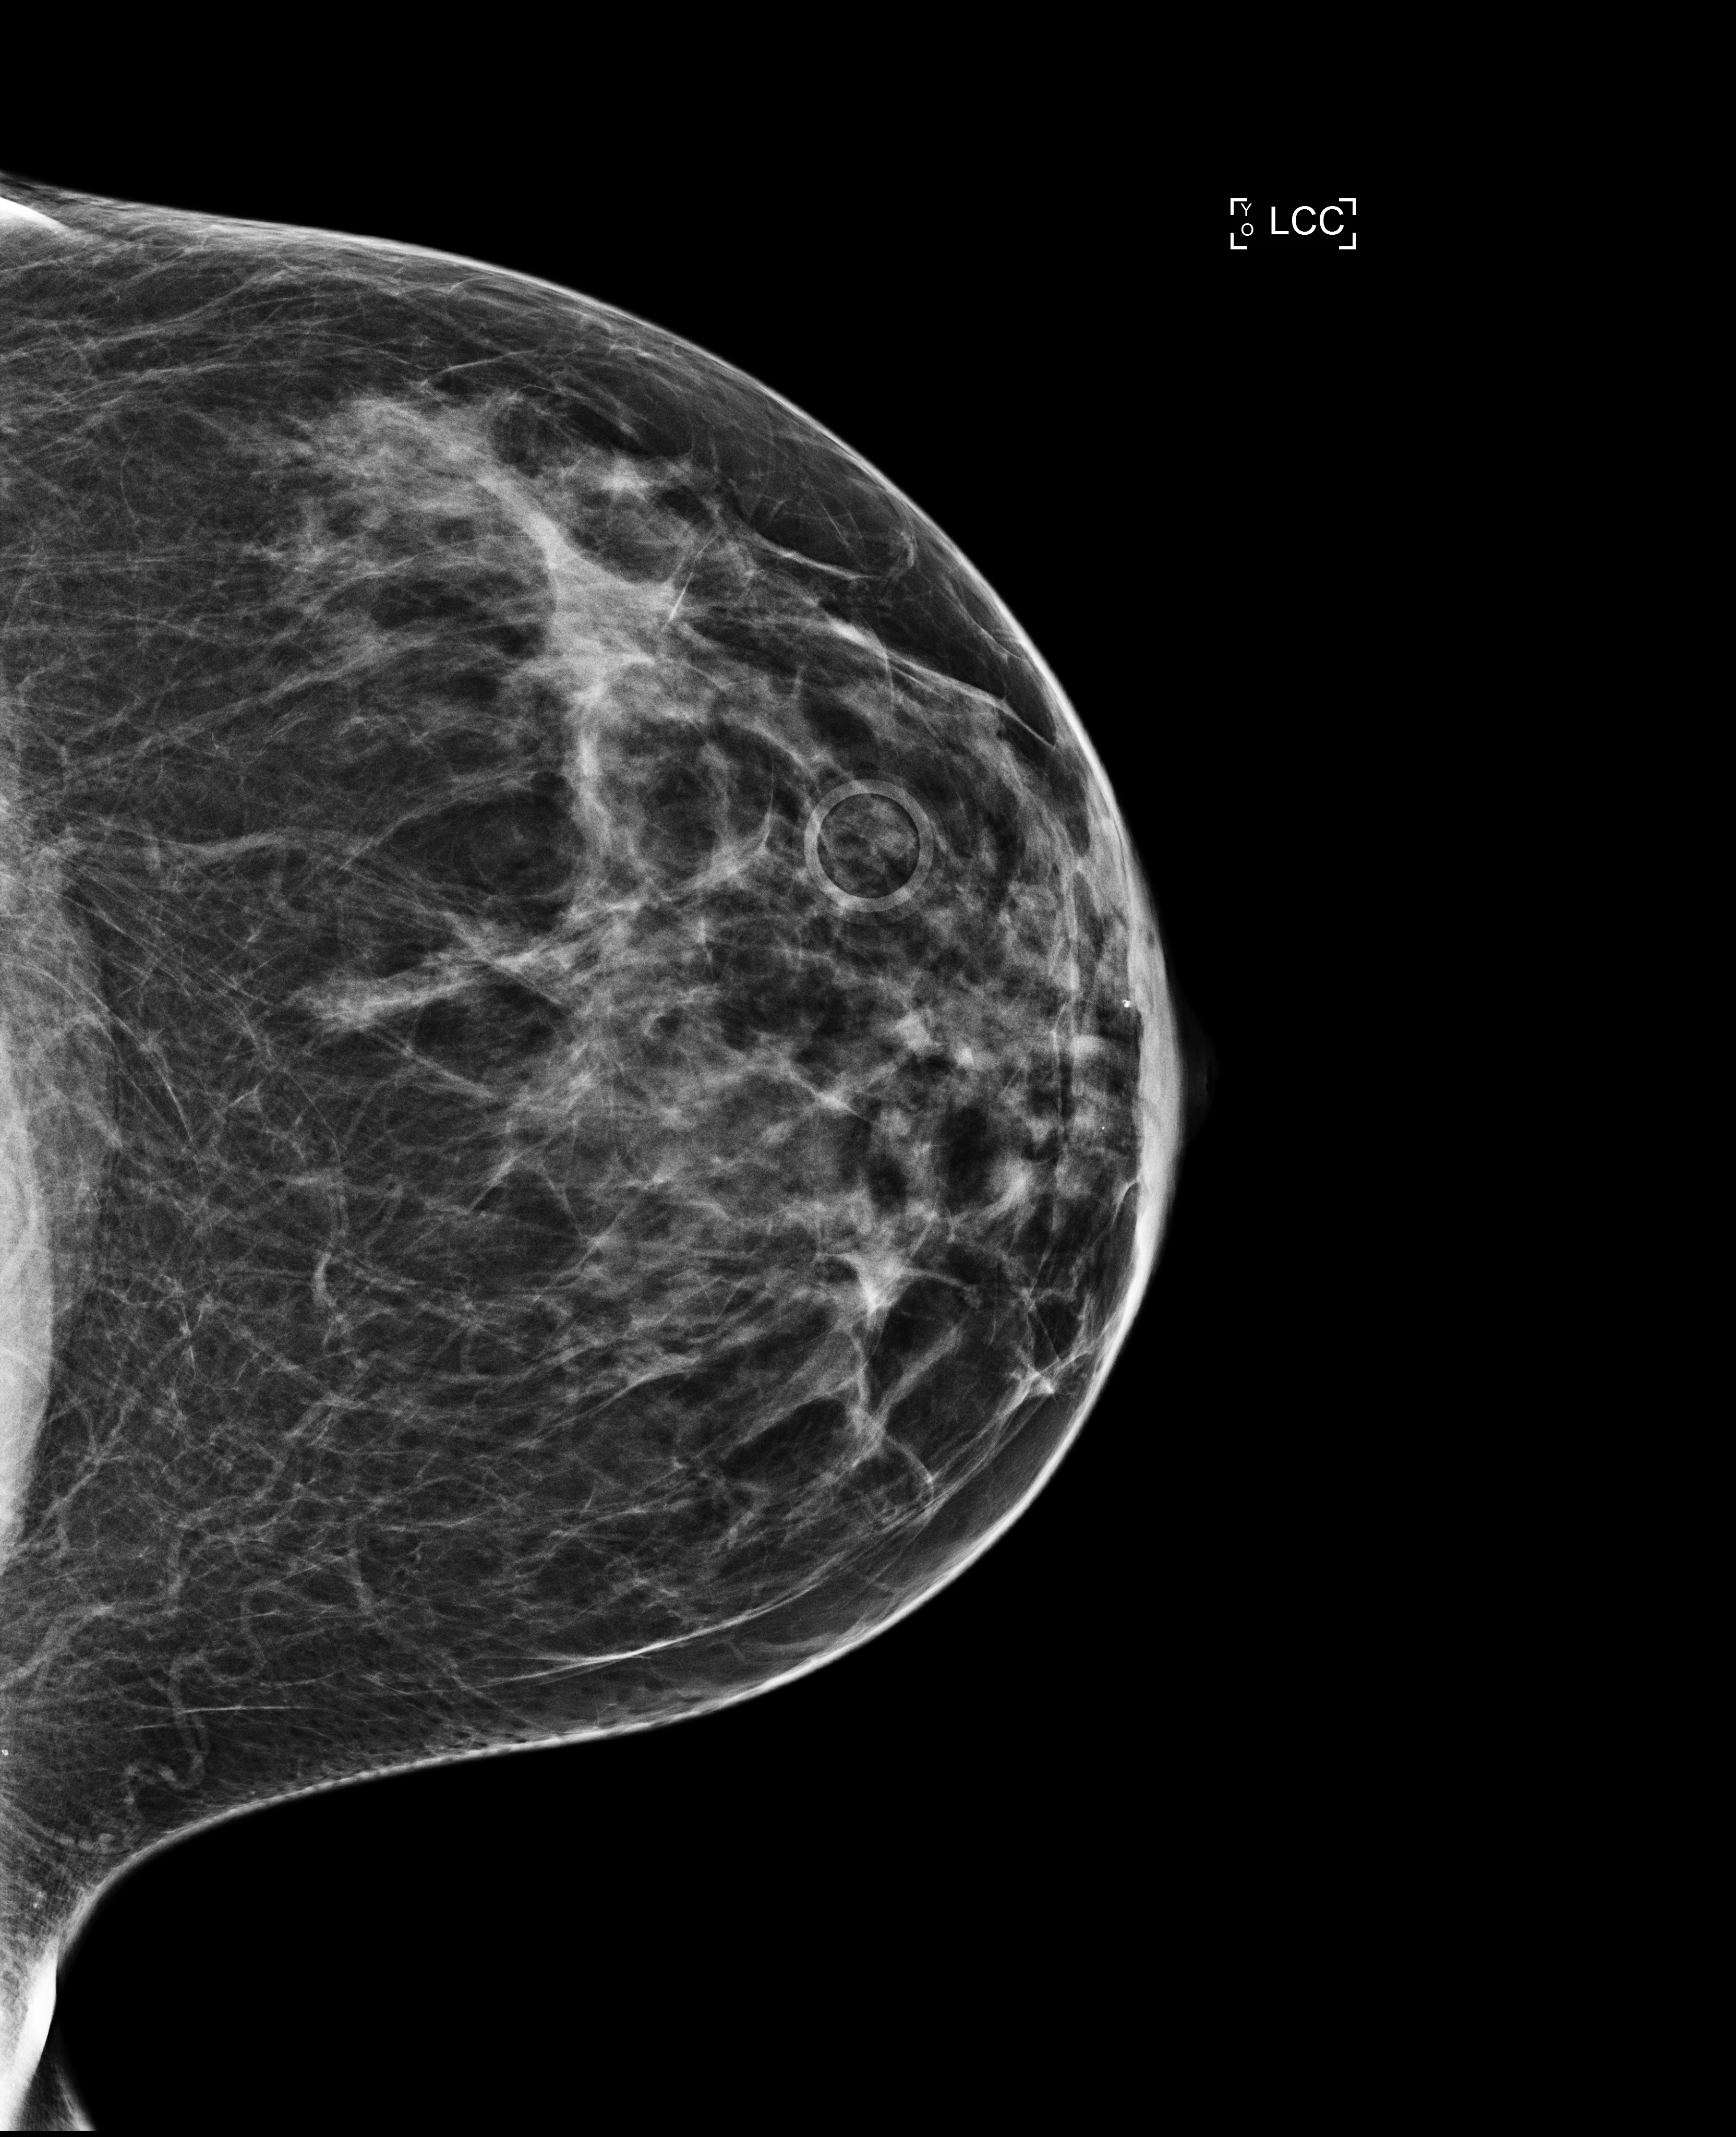
Digital mammogram (FFDM); left breast; craniocaudal (CC) view; annual screening mammography examination; compressed breast thickness 56 mm; system: Selenia Dimensions. Female patient, age 46 years.
Breast density at the screening exam (both breasts): heterogeneously dense (BI-RADS density category c). Final BI-RADS assessment for this screening round (tomosynthesis exam, both breasts): category 2. Recall: recalled for additional imaging after this screen.